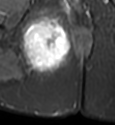
MRI of an extremity soft-tissue mass, one axial slice; position 27 of 49 along the scan axis; STIR; MR volume resampled by the dataset authors to the PET/CT grid (not the native acquisition matrix); 115 × 125 image matrix, field of view 112 × 122 mm. Female patient. Case-level facts recorded for this patient, not image findings: histological type: epithelioid sarcoma; grade: intermediate; site of the primary tumour: right buttock.
Outlined on this slice (expert contour drawn on MRI and transferred to this co-registered scan by the dataset authors):
- gross tumour volume including surrounding oedema: bounding box [x1, y1, x2, y2] px = [20, 14, 71, 72]
- gross tumour volume (mass): [24, 23, 68, 67]